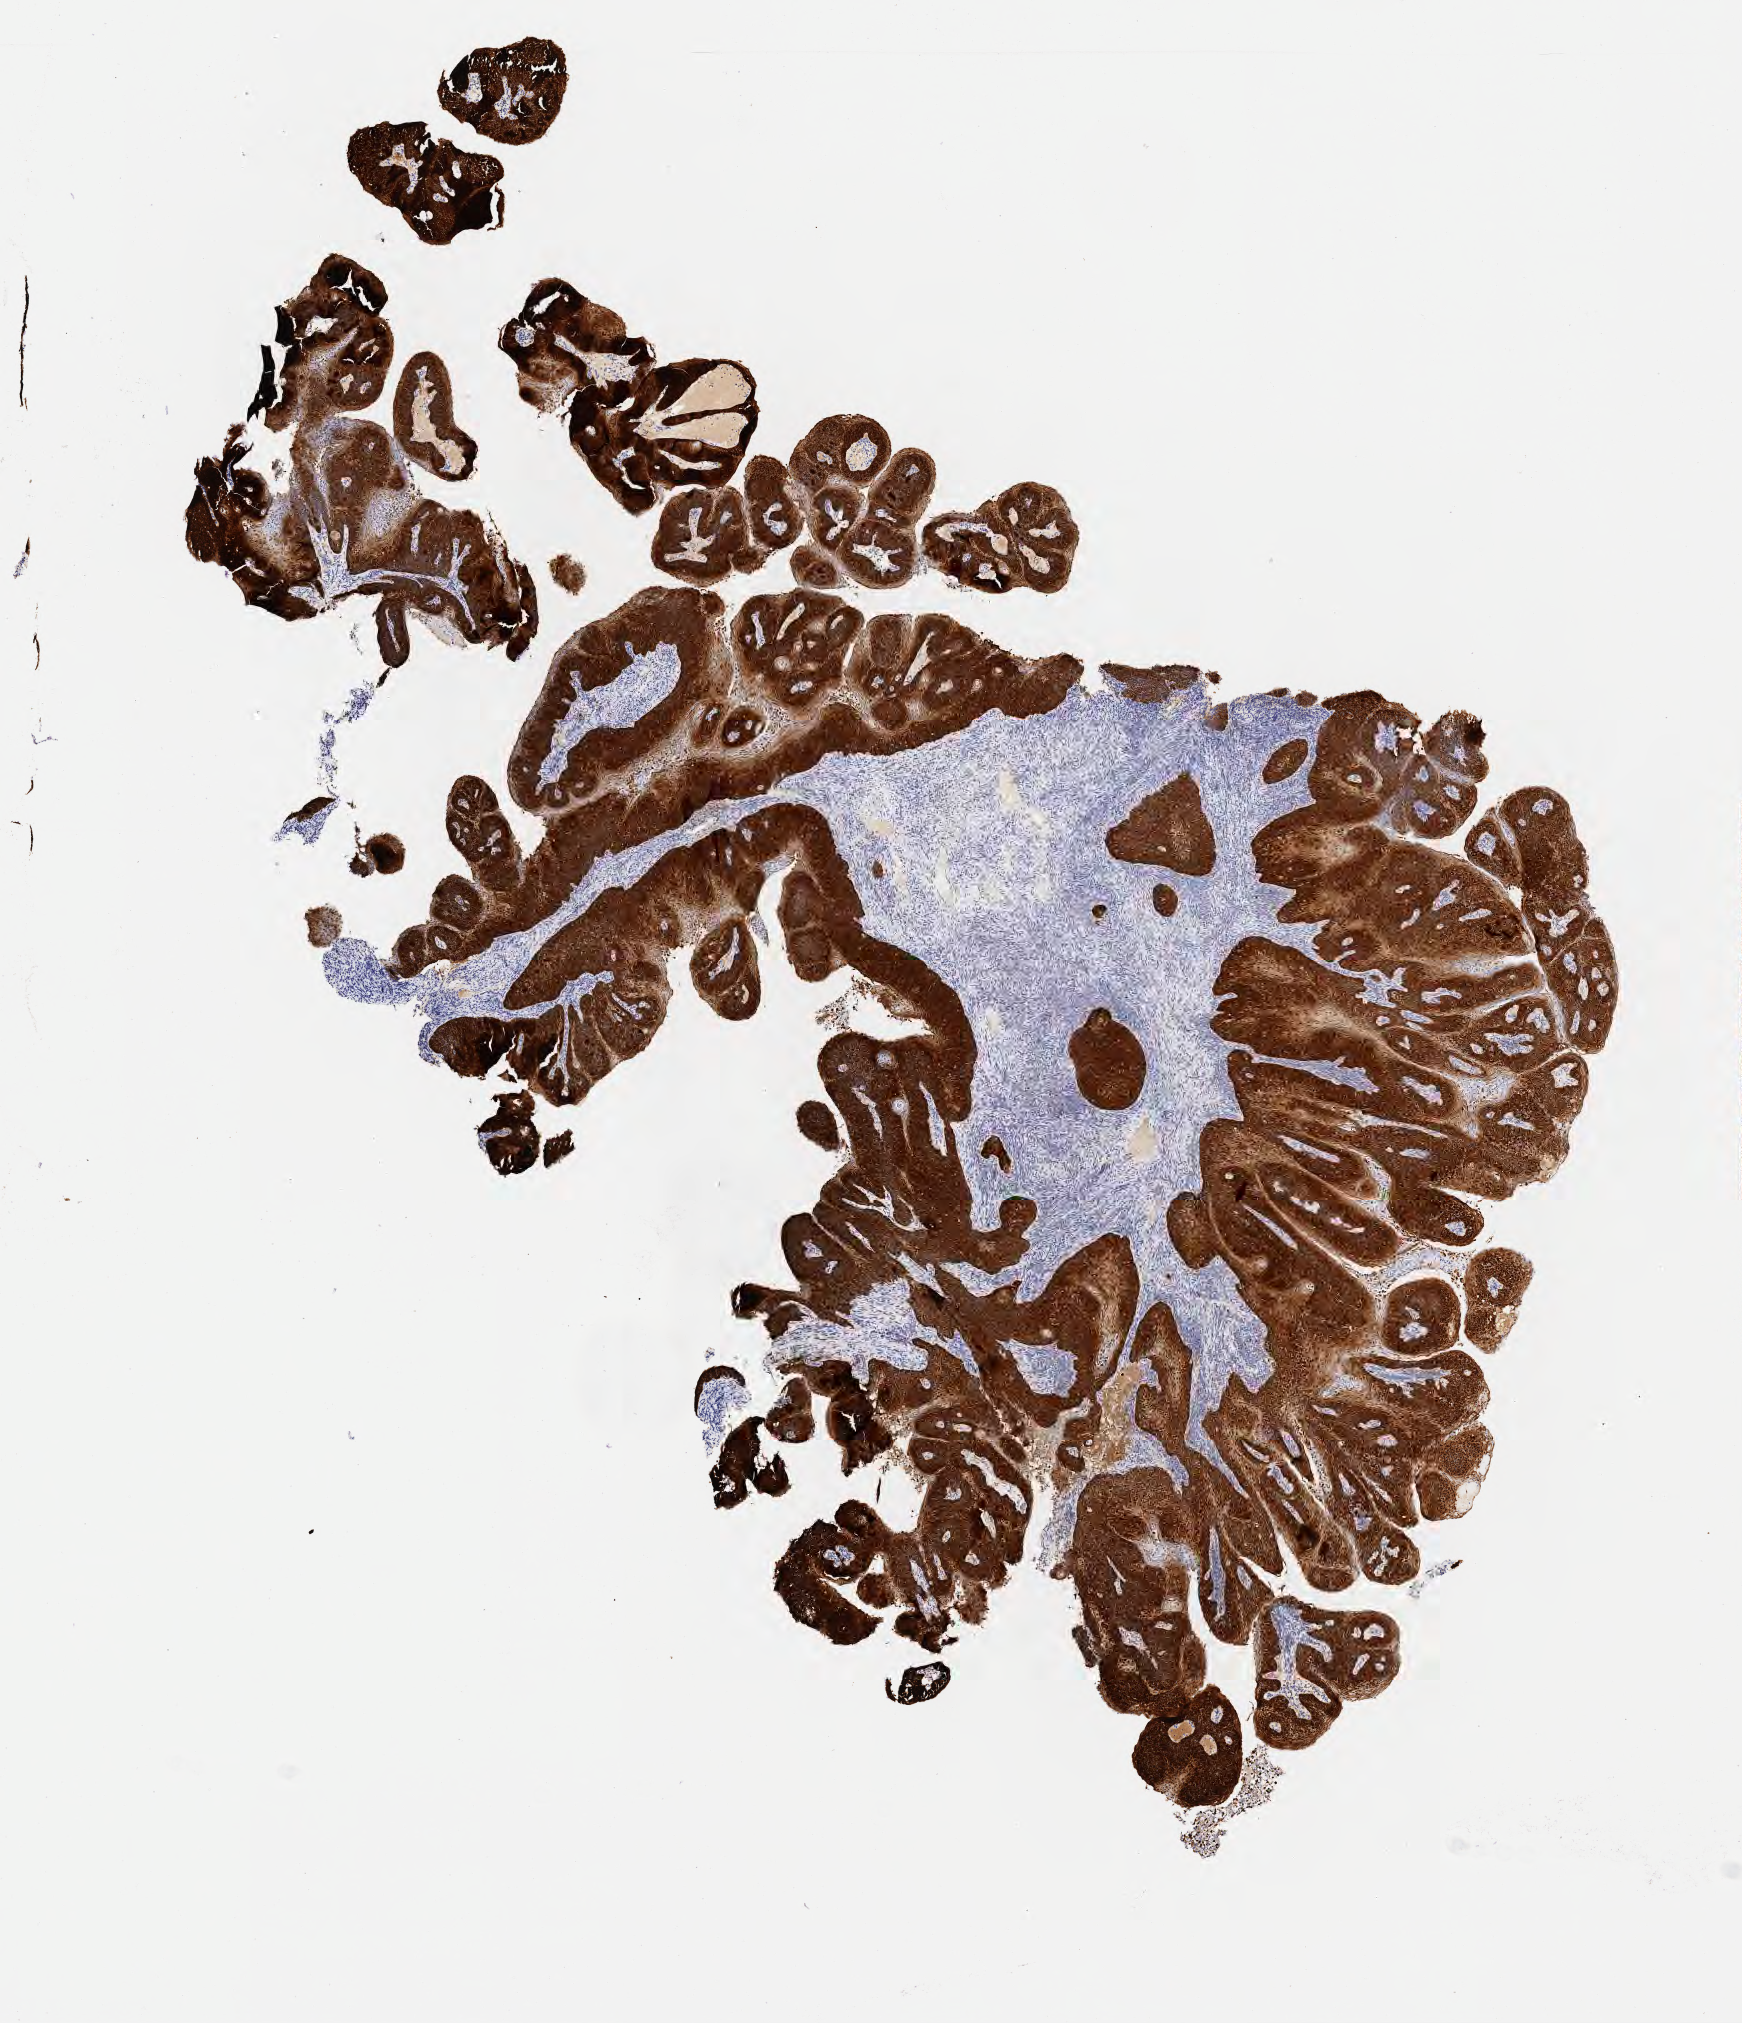
Immunohistochemistry (IHC) whole-slide image stained for p16 (p16INK4a) — whole scanned area (about 7.0 x 8.2 mm) shown as a low-resolution overview. Tumor tissue. Site: cervix. Patient: female, 40 years old.
* histologic diagnosis: Squamous cell carcinoma, NOS